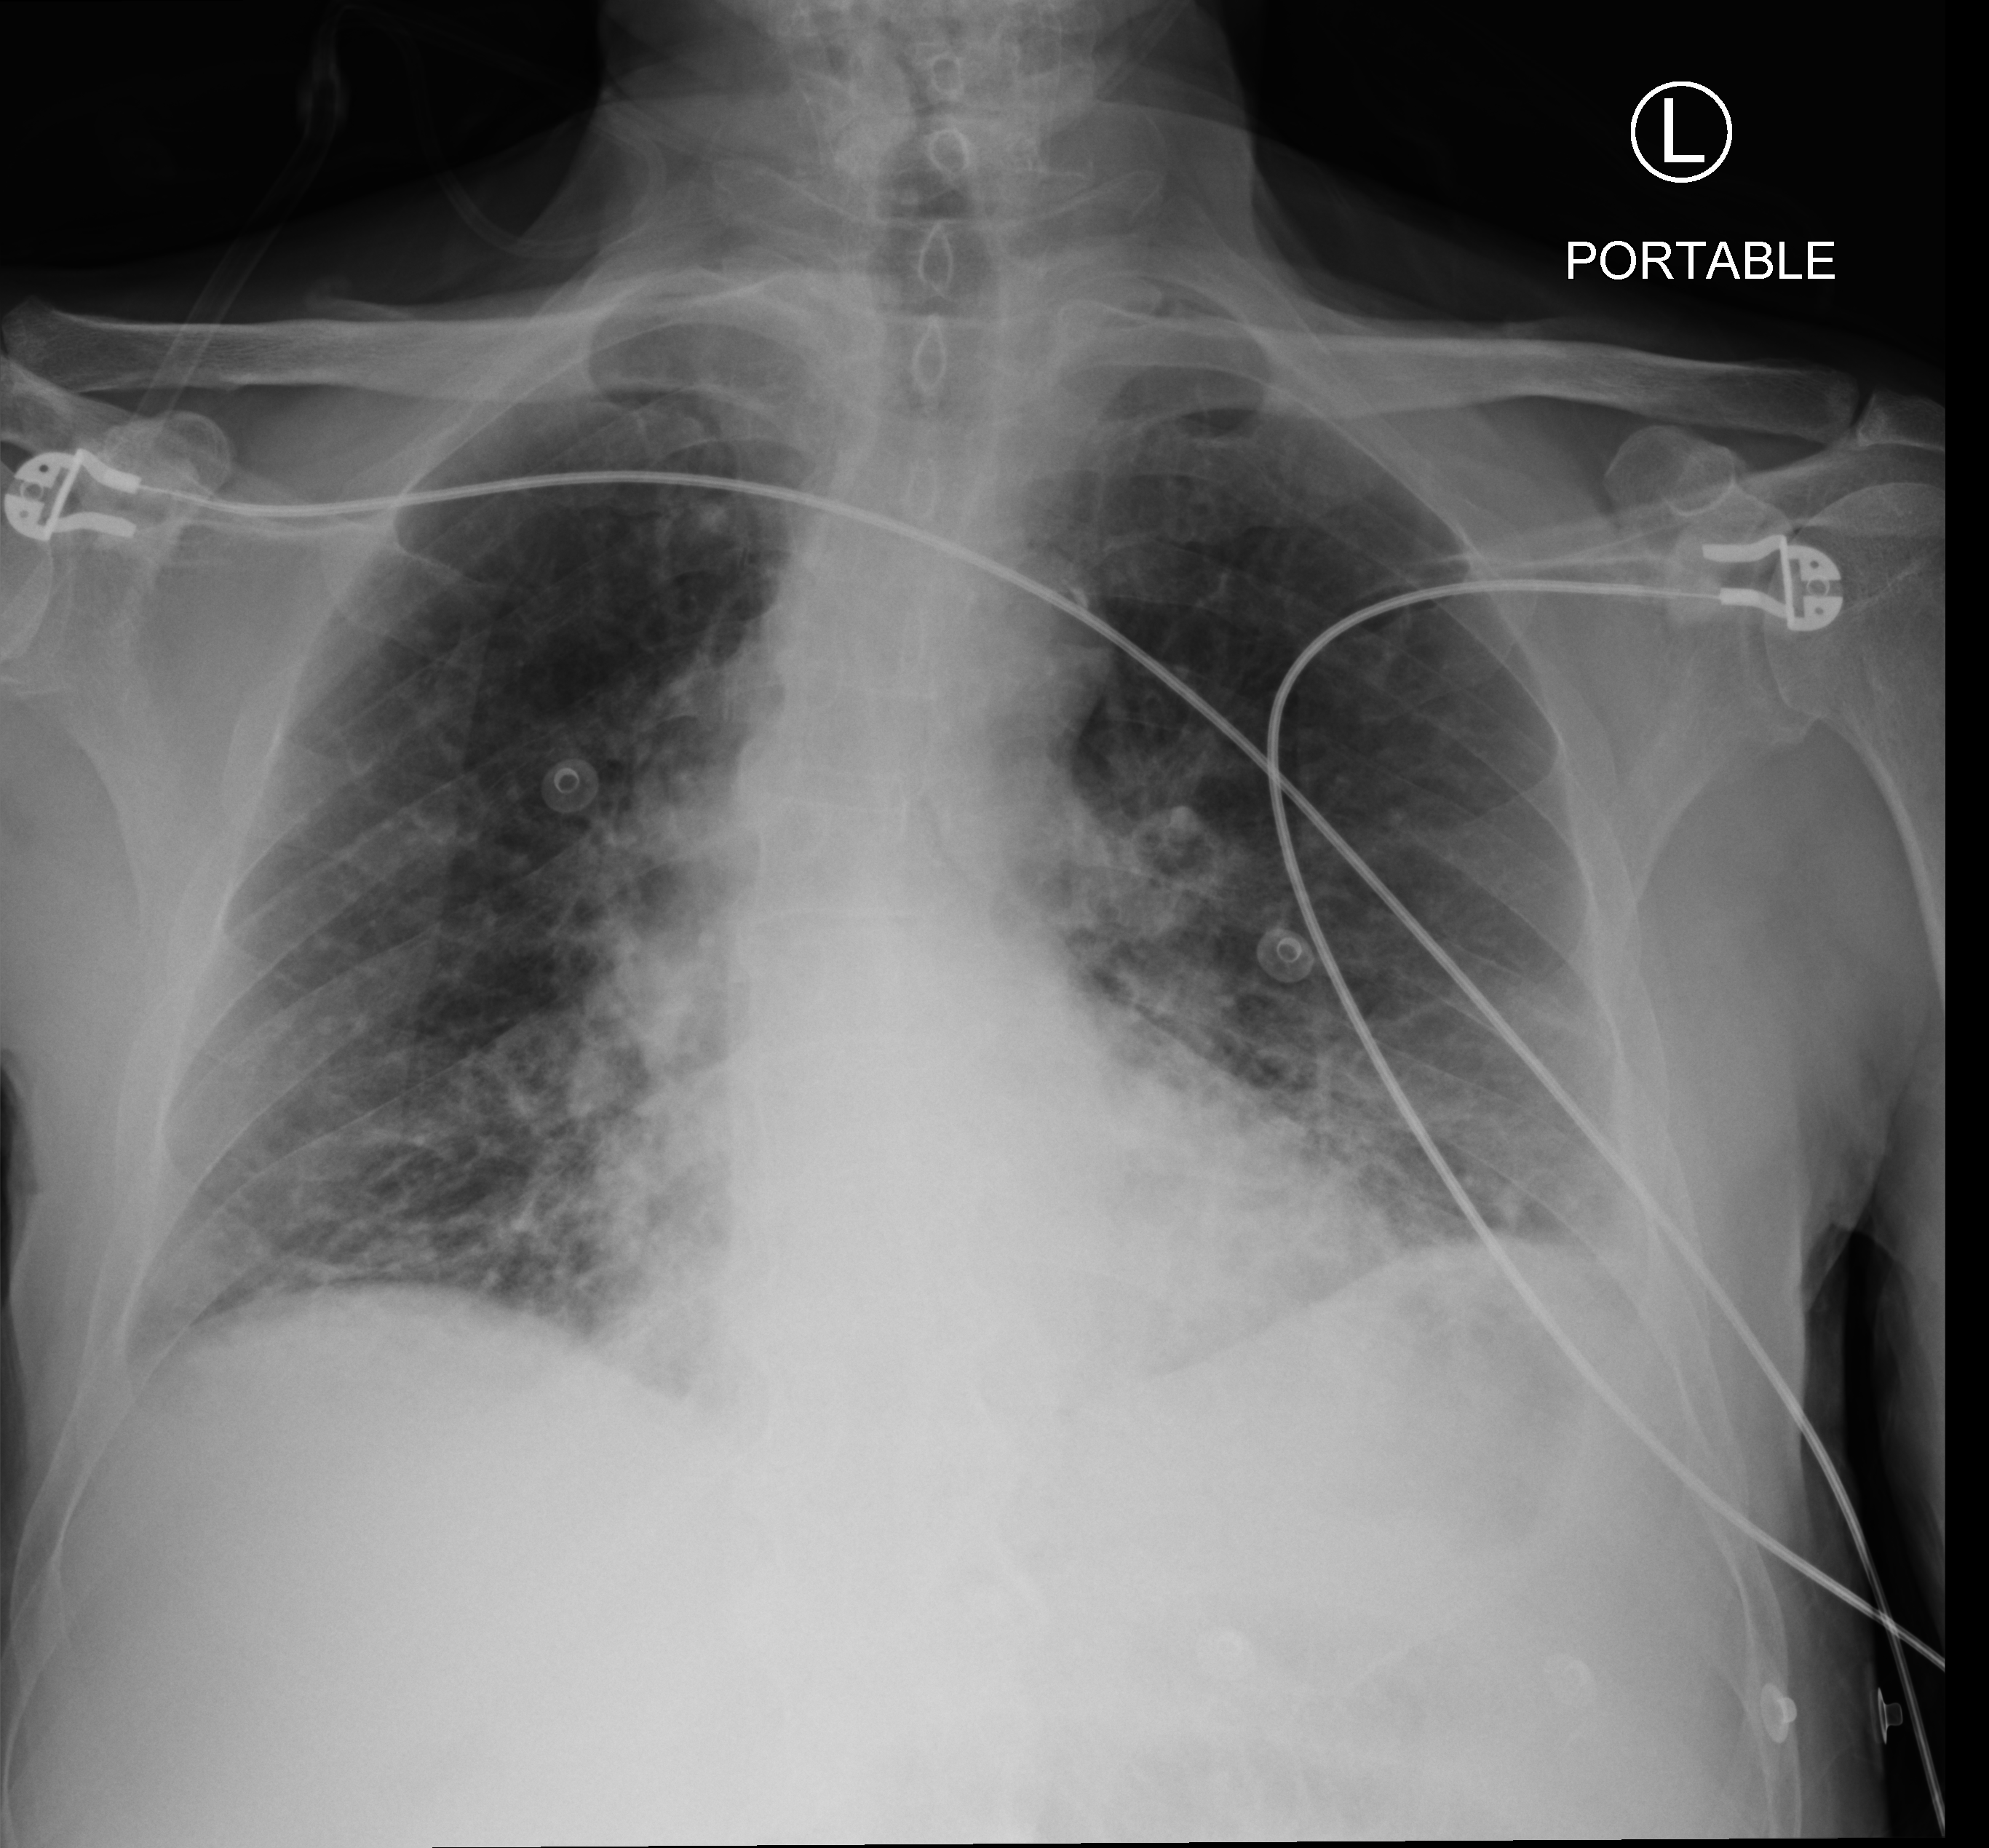
Portable chest radiograph. Patient hospitalised with COVID-19; male, aged 75–90 years.
From the hospital-stay record, not from the radiograph (when in the stay this image was taken is not recorded): hypertension (admission record): yes; admitted to intensive care during this hospital stay: no; COPD (admission record): no.